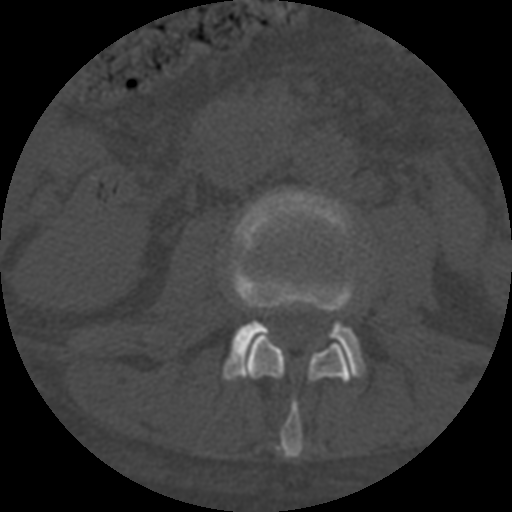
CT including the spine, one axial slice; slice 246 of 708 in the series (ordered by position); one of 3 acquisitions stored at this slice position; bone window (W 1800 / L 400 HU); 512 × 512 image matrix. Patient age 55 years. From the clinical record (not read from this slice): primary cancer: colon; vertebrae with lytic lesions (as recorded): T12, L1, L5.
Annotated regions visible in this slice (semi-automatic segmentation, software-assisted and operator-edited):
- L2 vertebra: bounding box [x1, y1, x2, y2] px = [244, 336, 352, 459]
- L3 vertebra: [224, 192, 364, 379]